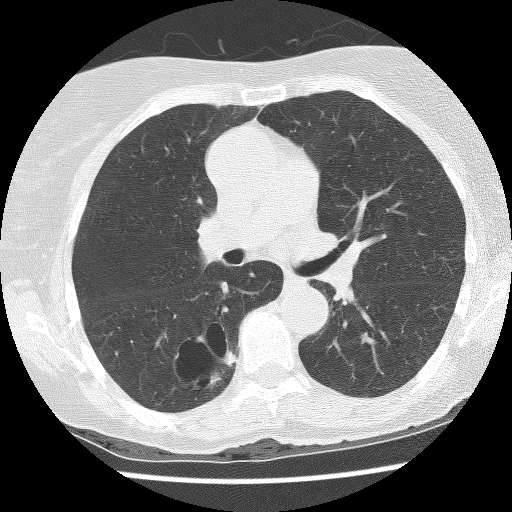
Low-dose screening chest CT, axial slice; baseline screening round; lung window (W 1500 / L -600 HU); 2.5 mm slice thickness; slice 54 of 136 in the series; 512 × 512 image matrix. Female participant, aged 69 years at enrolment. Former smoker at enrolment.
Lesion marked by an expert reader, bounding box [x1, y1, x2, y2] px = [157, 319, 248, 394]. The screening reader recorded 2 non-calcified nodules or masses ≥4 mm on this exam (right lower lobe, right lower lobe); which of them this box marks is not recorded. Participant outcome: lung cancer diagnosed 288 days after this screen — non-small cell carcinoma, right lower lobe, poorly differentiated (G3), stage IB (AJCC 6th edition), 36 mm at pathology.